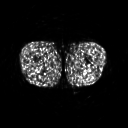
FDG PET of an extremity soft-tissue mass (from a PET/CT study), one axial slice. Slice 220 of 267 in the series (ordered by position). 3.27 mm slice thickness. 128 × 128 image matrix. Patient: male, 27 years. From the clinical record (not read from this slice): histological type: extraskeletal osteosarcoma; grade: high; site of the primary tumour: left adductur.
Annotated regions visible in this slice (expert contour drawn on MRI and transferred to this co-registered scan by the dataset authors):
- gross tumour volume (mass): bounding box <70,62,90,70> (left, top, right, bottom; pixels)